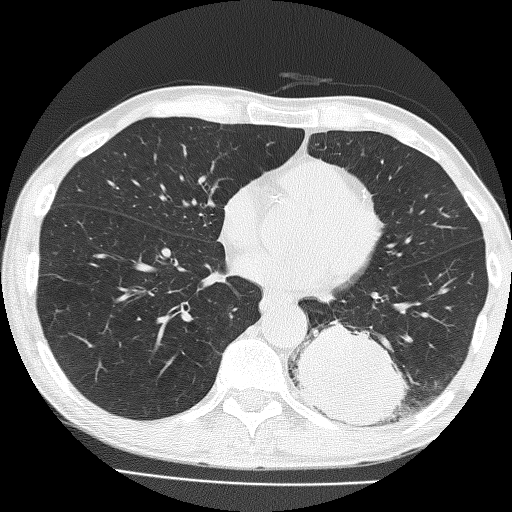
Low-dose screening chest CT, axial slice, baseline annual screen, lung window (W 1500 / L -600 HU), lung (sharp) reconstruction kernel (FC51). Male, age 58 years at enrolment. Current smoker at enrolment.
- Lesion marked by an expert reader, bounding box <298,306,423,434> (left, top, right, bottom; pixels).
- The screening reader recorded 2 non-calcified nodules or masses ≥4 mm on this exam; which of them this box marks is not recorded.
- Later outcome: lung cancer diagnosed 39 days after this screen — non-small cell carcinoma, left lower lobe, poorly differentiated (G3), stage IV (AJCC 6th edition), 74 mm at pathology.